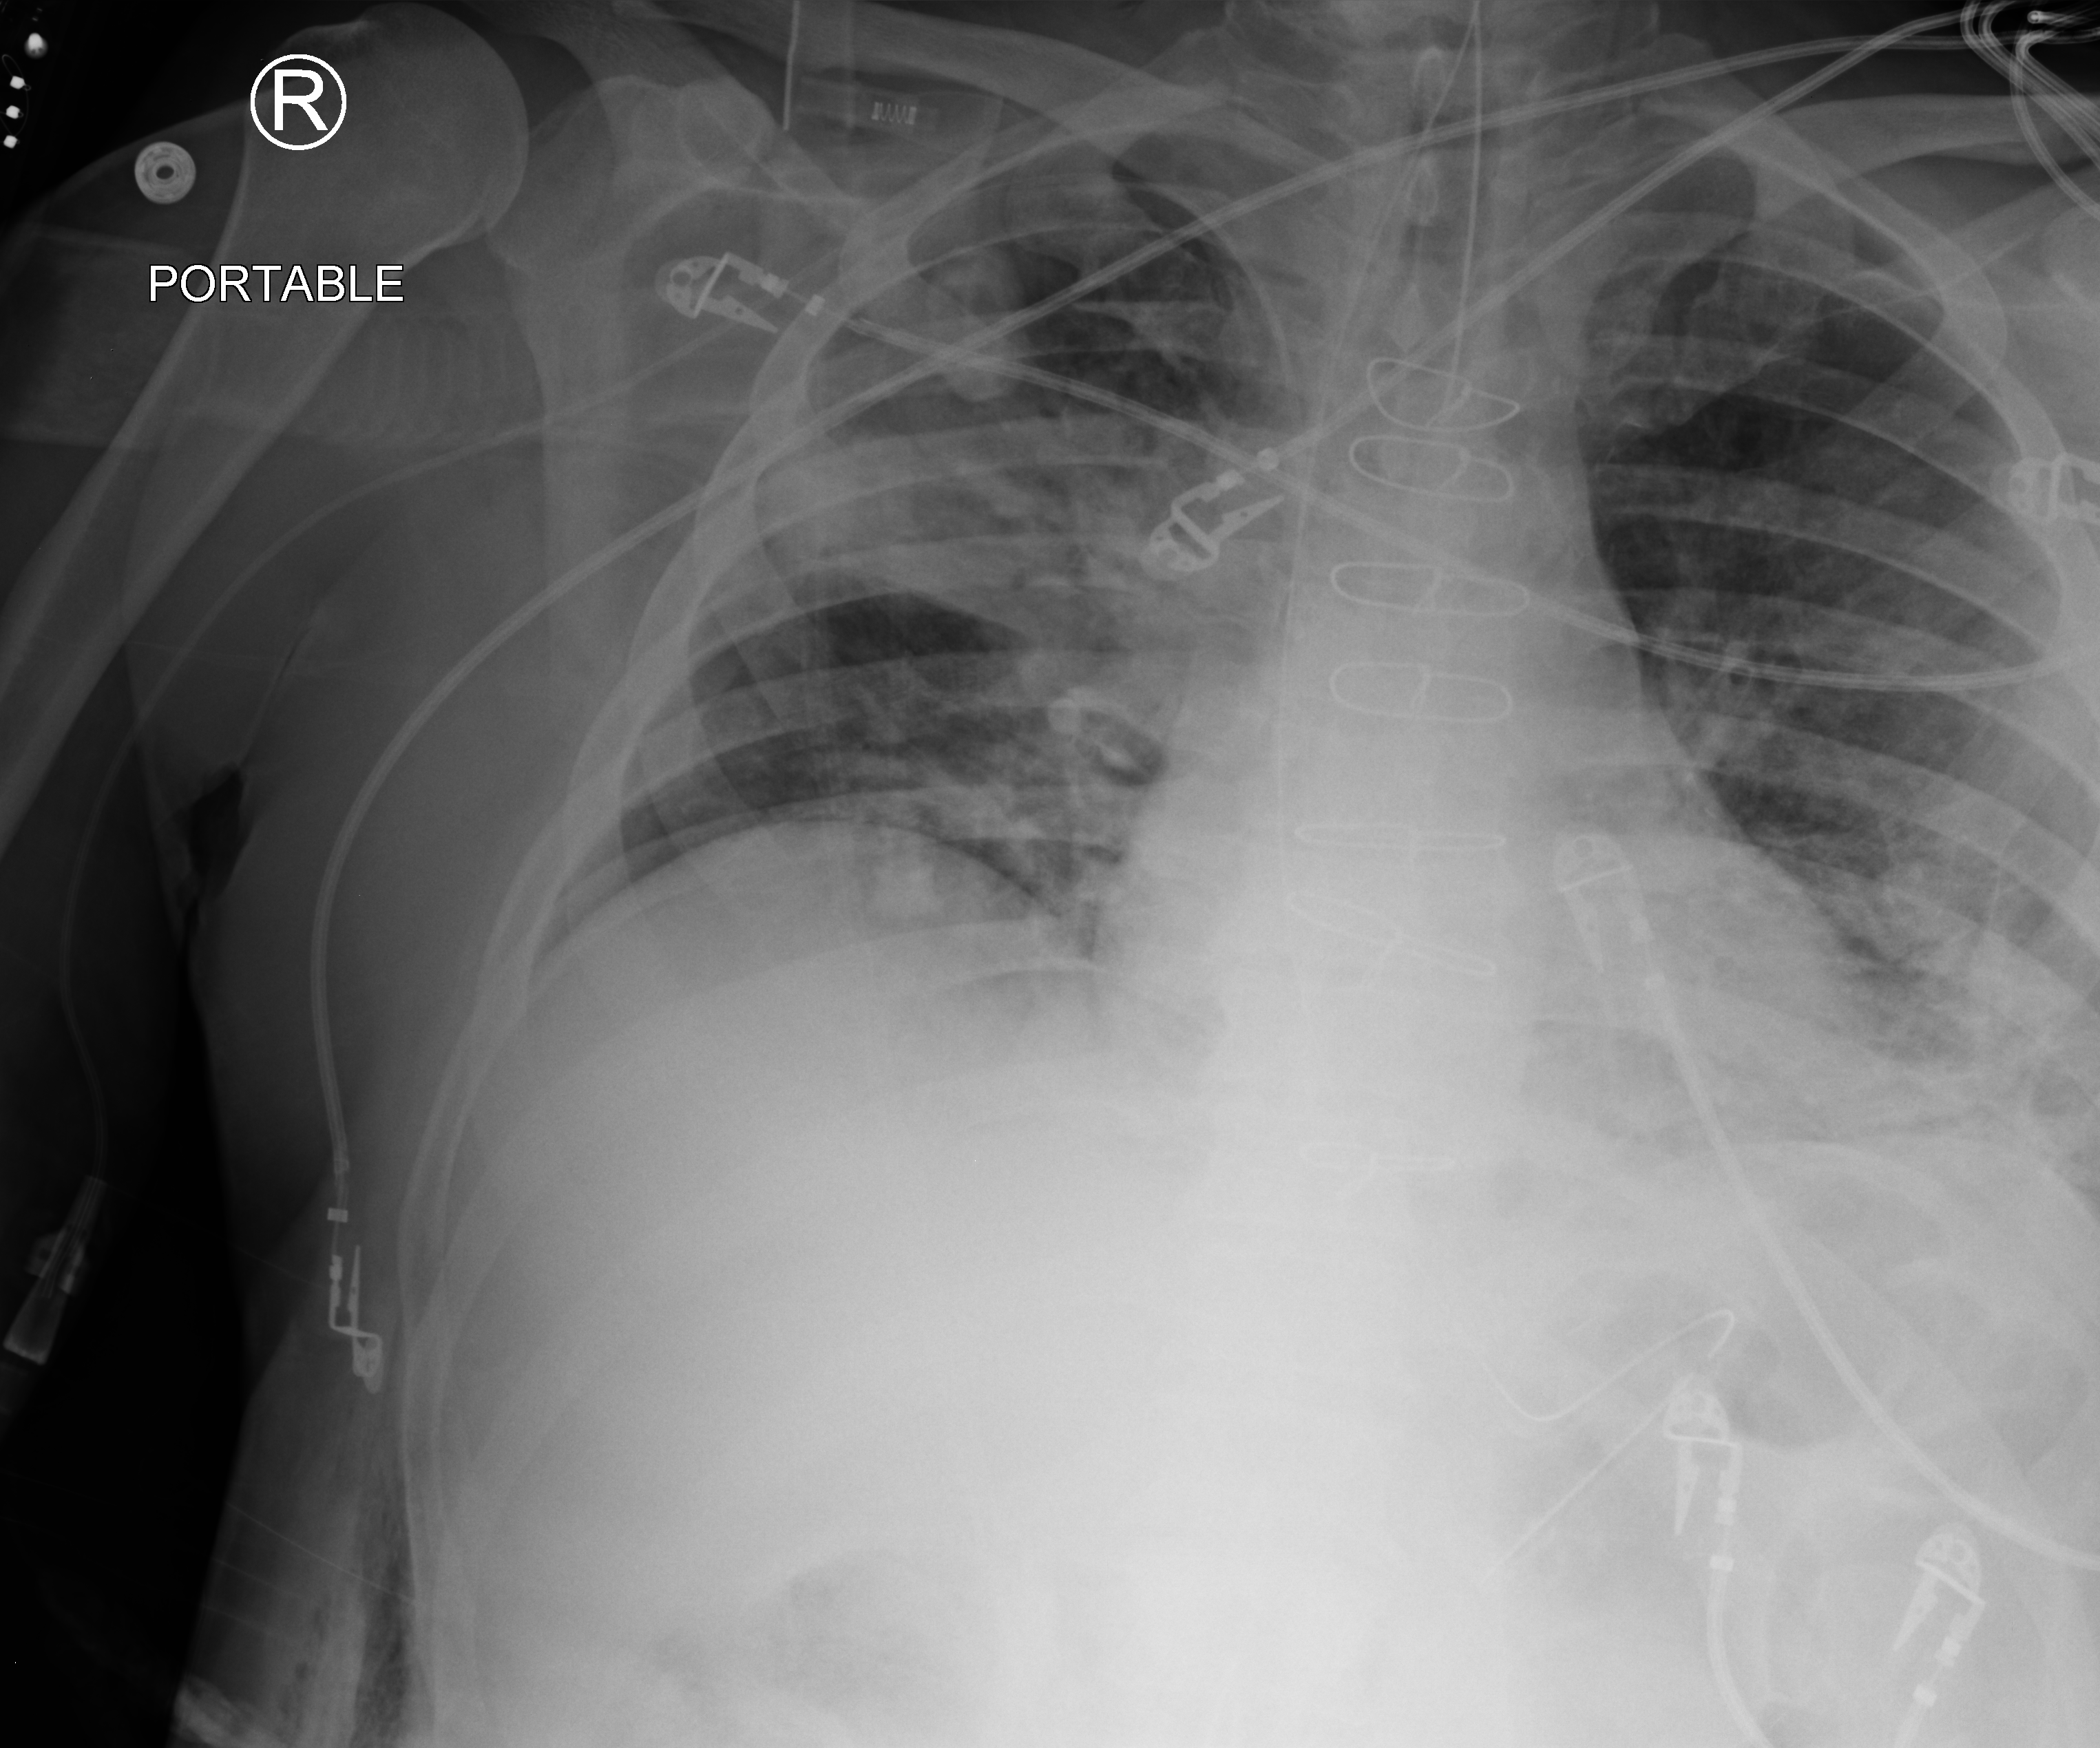
Portable chest radiograph, anteroposterior (AP) projection. Male patient hospitalised with COVID-19, age 60–74 years.
Admission-level facts for this patient (not findings on this image; timing relative to this image not recorded):
- admitted to intensive care during this hospital stay: yes